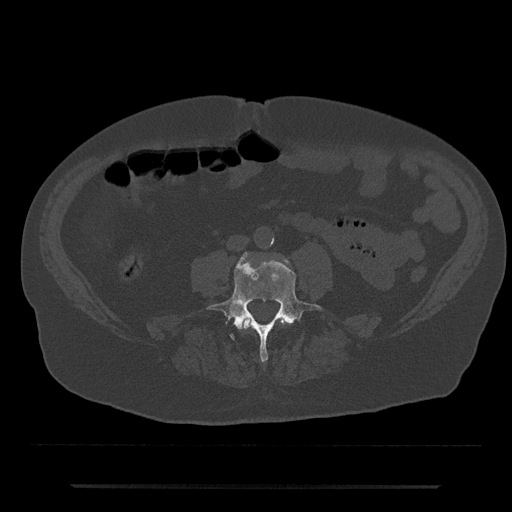
CT including the spine, one axial slice. Bone window (W 1800 / L 400 HU). 0.5 mm slice thickness. 512 × 512 image matrix, field of view 434 × 434 mm. Male patient, age 80 years. Case-level facts recorded for this patient, not image findings: primary cancer: prostate.
Annotated regions visible in this slice (semi-automatically segmented with operator editing):
- L3 vertebra: bounding box <242,318,289,330> (left, top, right, bottom; pixels)
- L4 vertebra: <207,253,322,362>